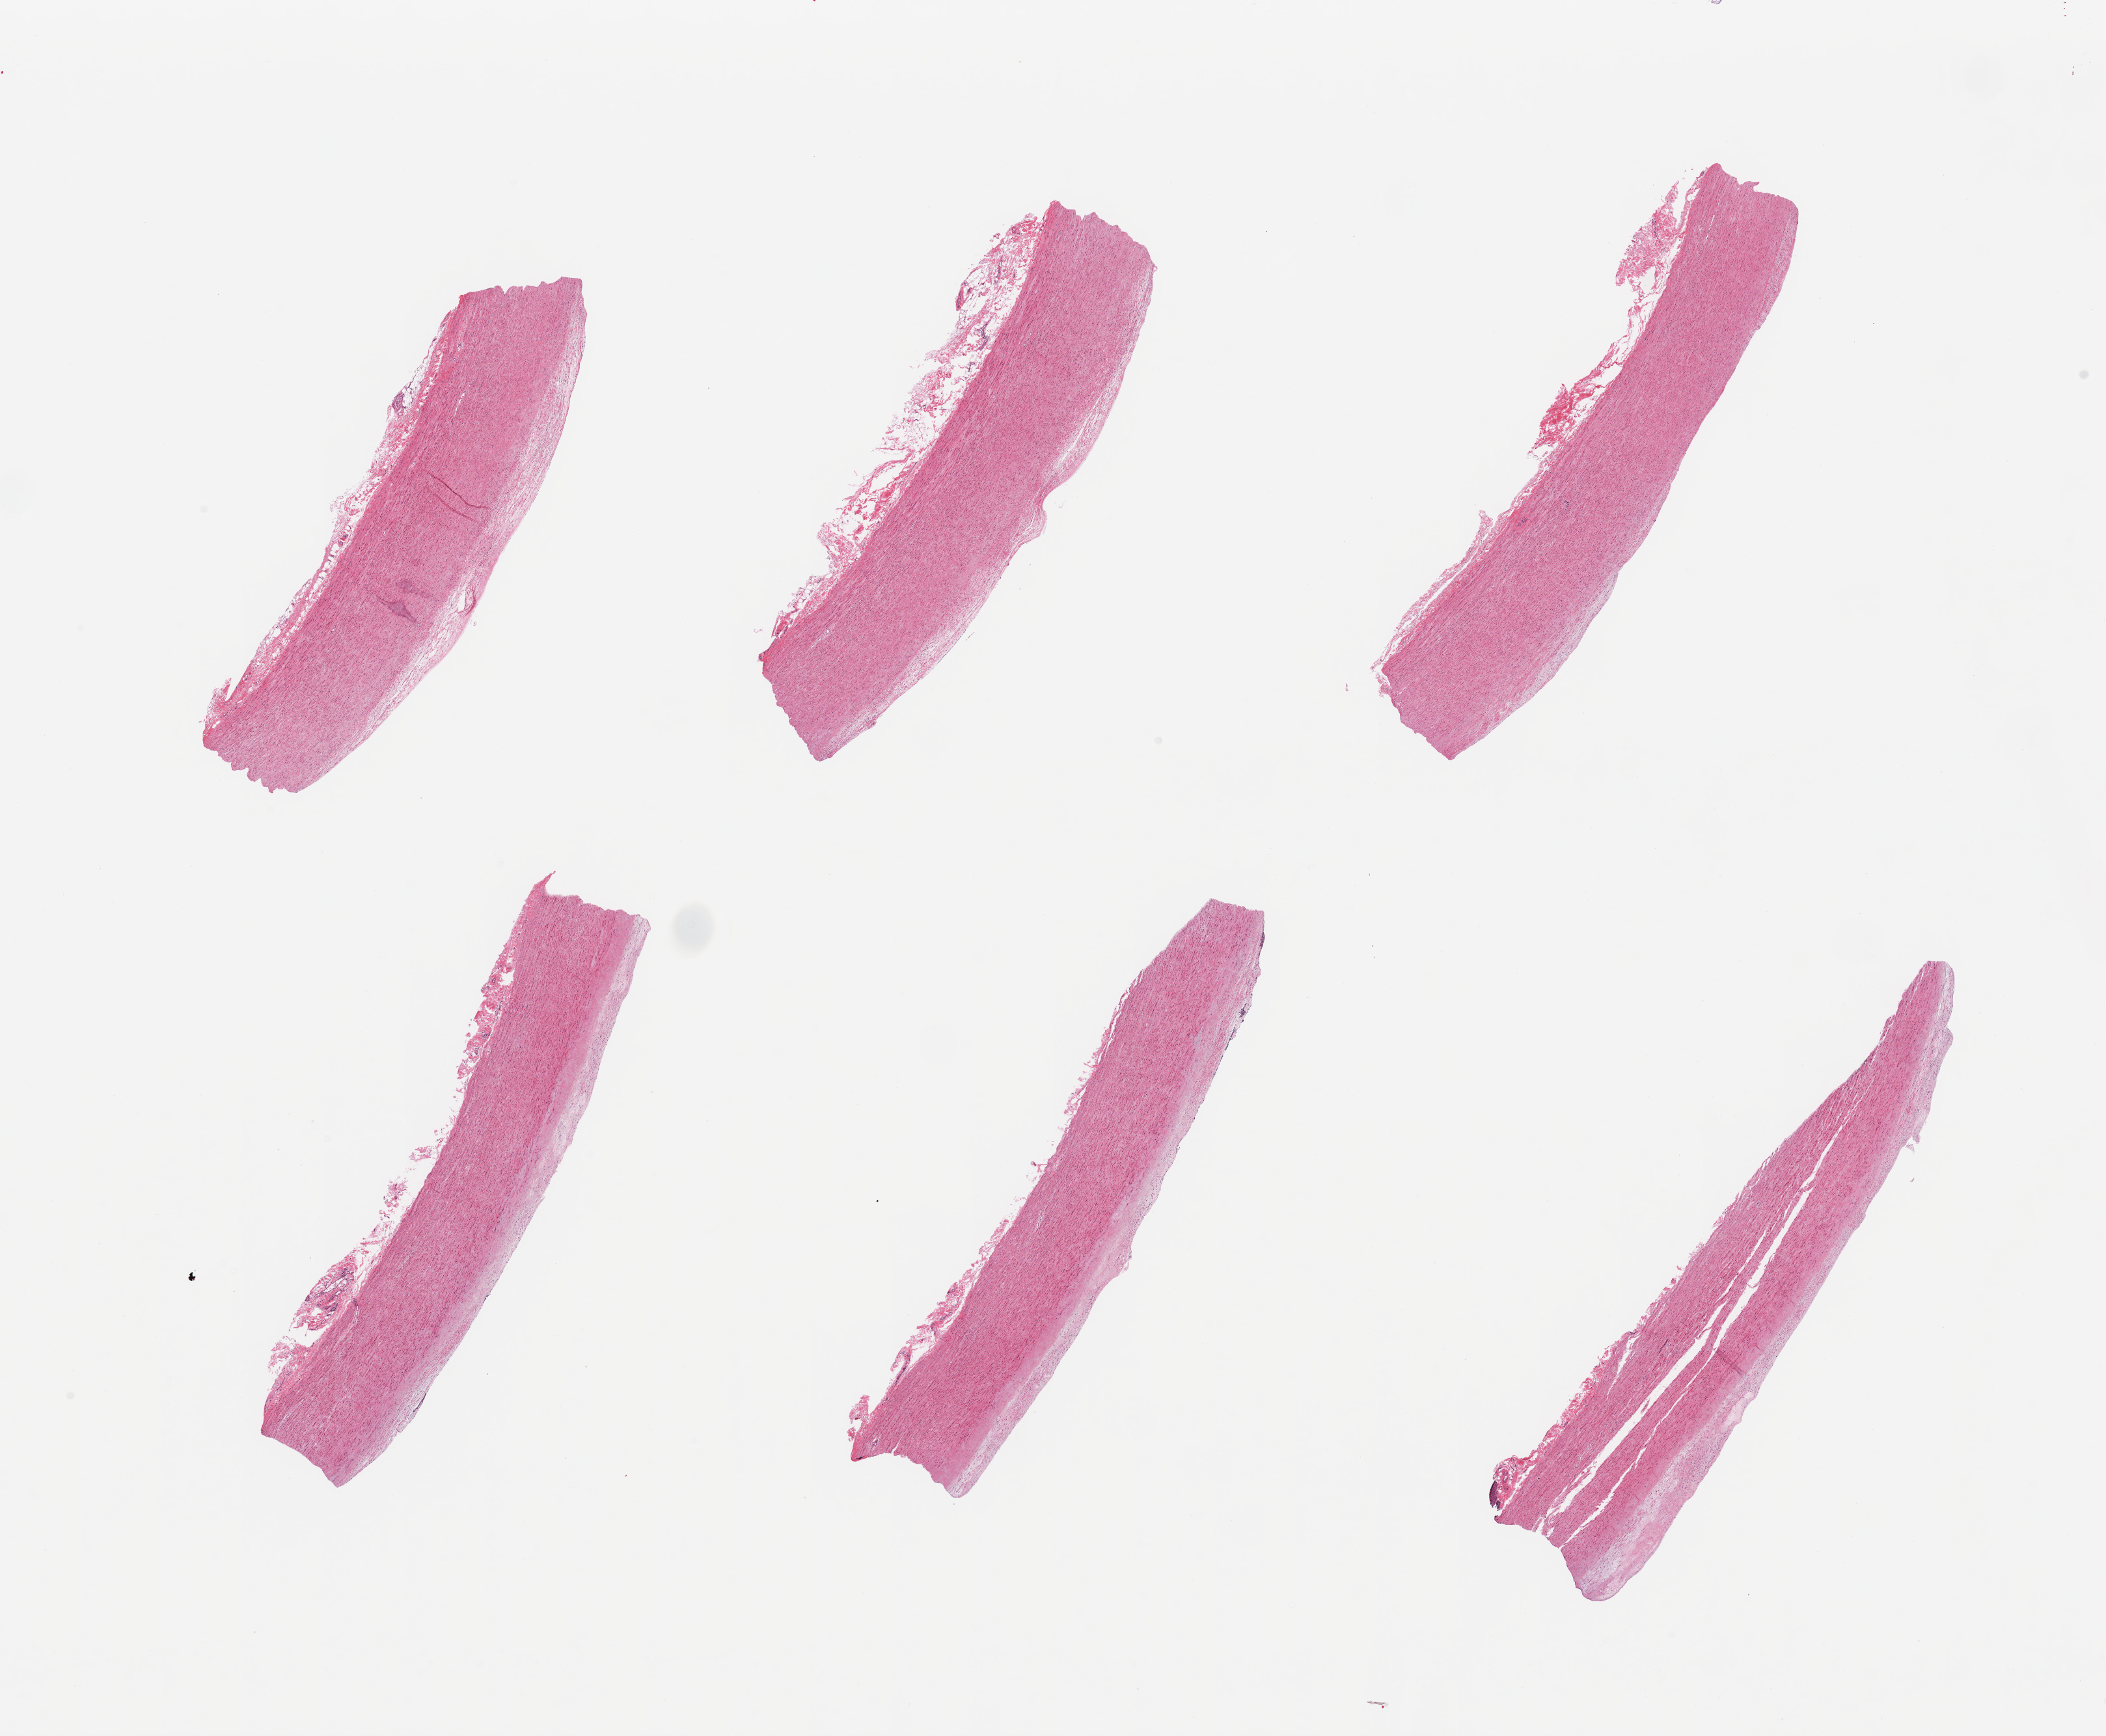
Digitized haematoxylin and eosin-stained section, a low-resolution overview of the entire scanned area, about 25.6 x 21.1 mm; PAXgene-fixed paraffin-embedded (PFPE) section; section of aorta (target tissue); donor tissue sample. Donor sex: male.
Reviewer comment on this tissue sample: 6 pieces; atherosclerosis.